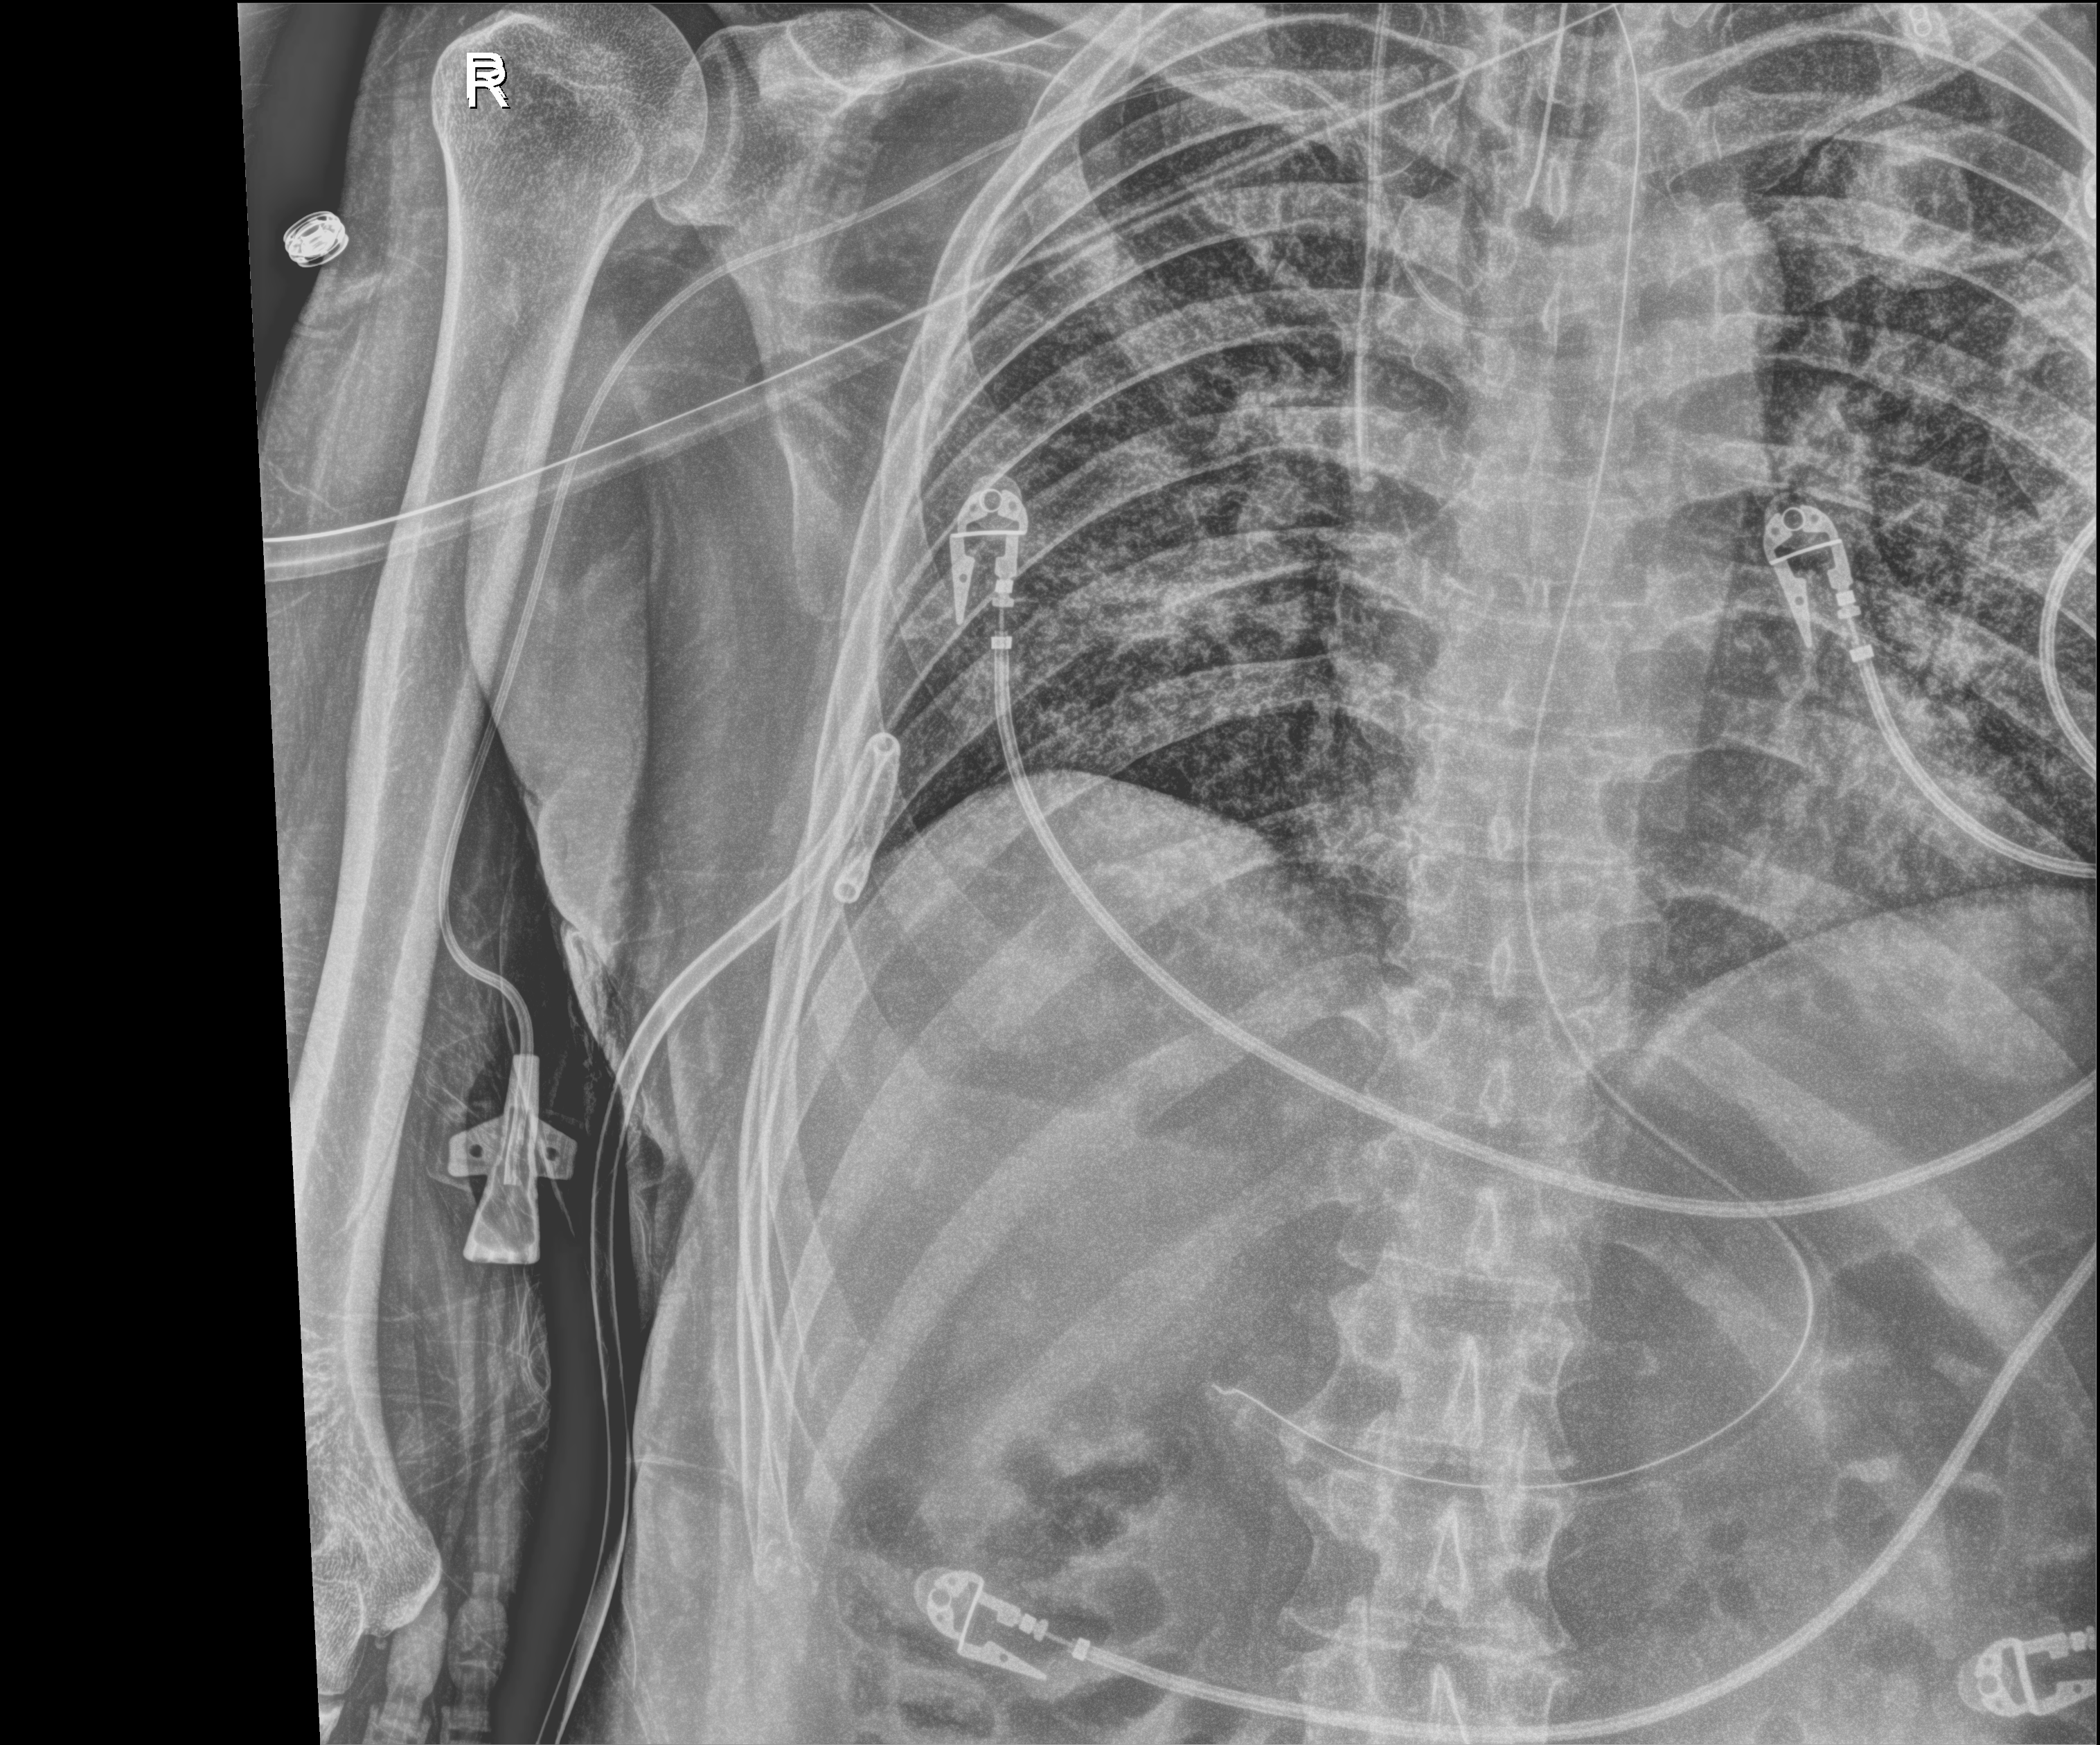
Bedside chest radiograph (digital radiography). Male patient hospitalised with COVID-19, age 18–59 years.
From the hospital-stay record, not from the radiograph (when in the stay this image was taken is not recorded): admitted to intensive care during this hospital stay: yes; length of hospital stay: 77 days.